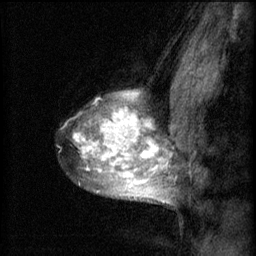
Breast MRI (dynamic contrast-enhanced), one sagittal slice. Slice 46 of 60 in the series (ordered by position). 3 images stored at this slice position (order not interpretable as contrast timing). 1.5 T. TE 4.2 ms, TR 8.2 ms. 2 mm slice thickness. 256 × 256 image matrix. Patient: female, 40 years.
Structures marked on this image (semi-automatically segmented with operator editing):
- analysis volume of interest (the breast-tissue region the enhancement analysis was run in; not a lesion): bounding box [x1, y1, x2, y2] px = [68, 84, 167, 205]
- tumour enhancement mask (voxels above the 70 % enhancement threshold inside the analysis volume of interest): [74, 92, 166, 203]